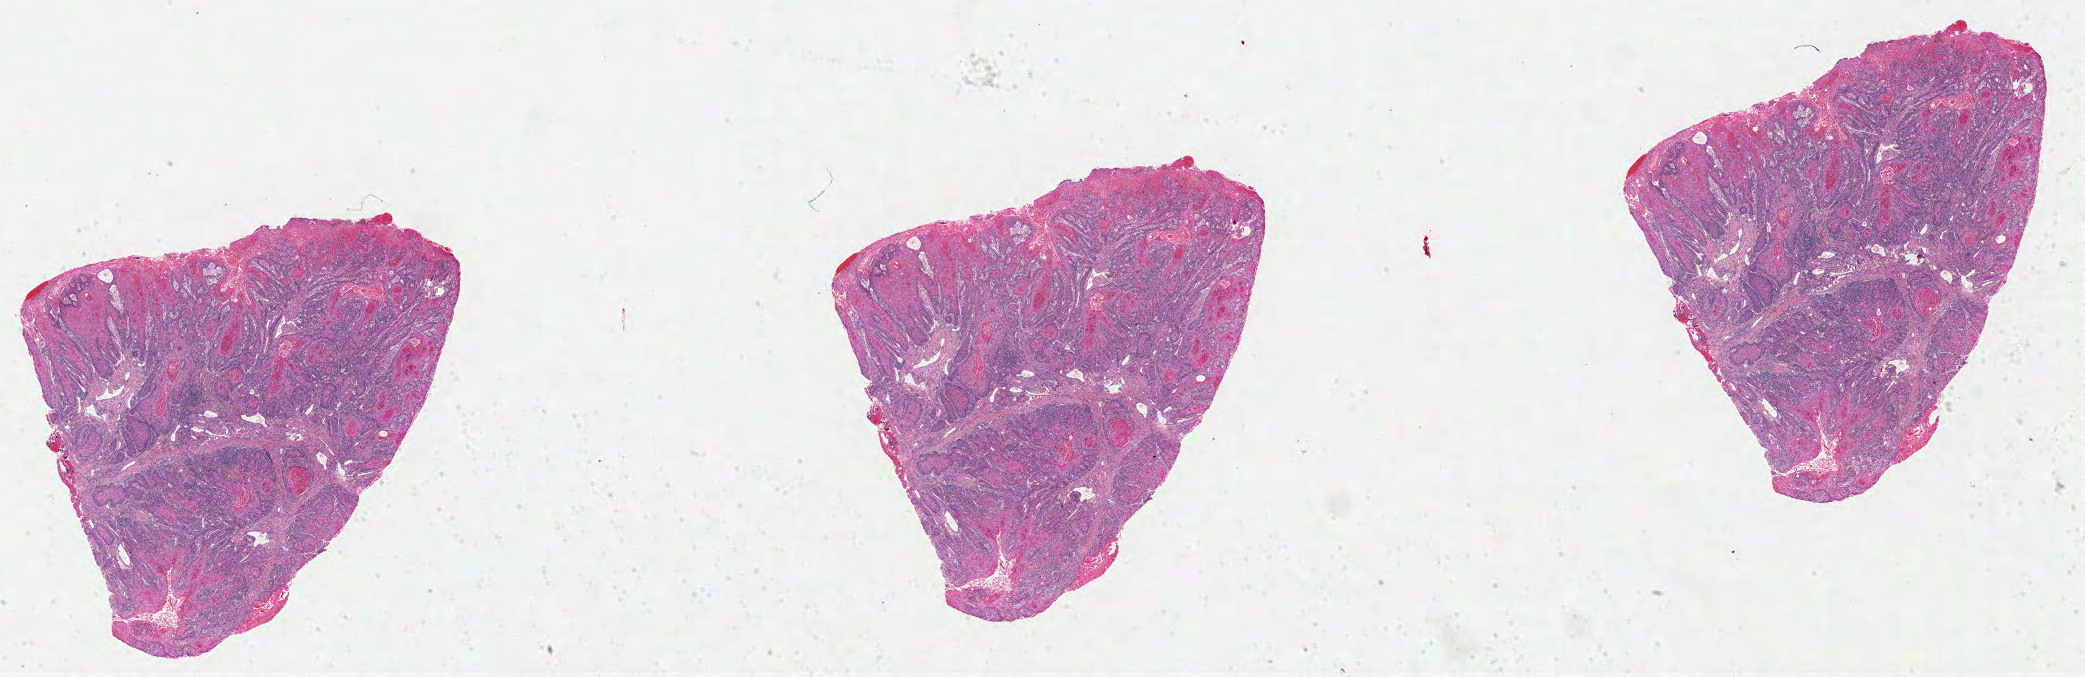
Whole-slide histology image, H&E, a low-resolution overview of the entire scanned area, about 32.8 x 10.6 mm (acquisition: 40x scan); formalin-fixed paraffin-embedded (FFPE) diagnostic section; head and neck, primary tumour sample. Male, age 65 years at initial diagnosis. Histologic grade: G1 (well differentiated).
- lymph nodes positive (case pathology): 0 of 37 examined
- pathologic diagnosis: Squamous cell carcinoma, NOS (overlapping lesion of lip, oral cavity and pharynx)